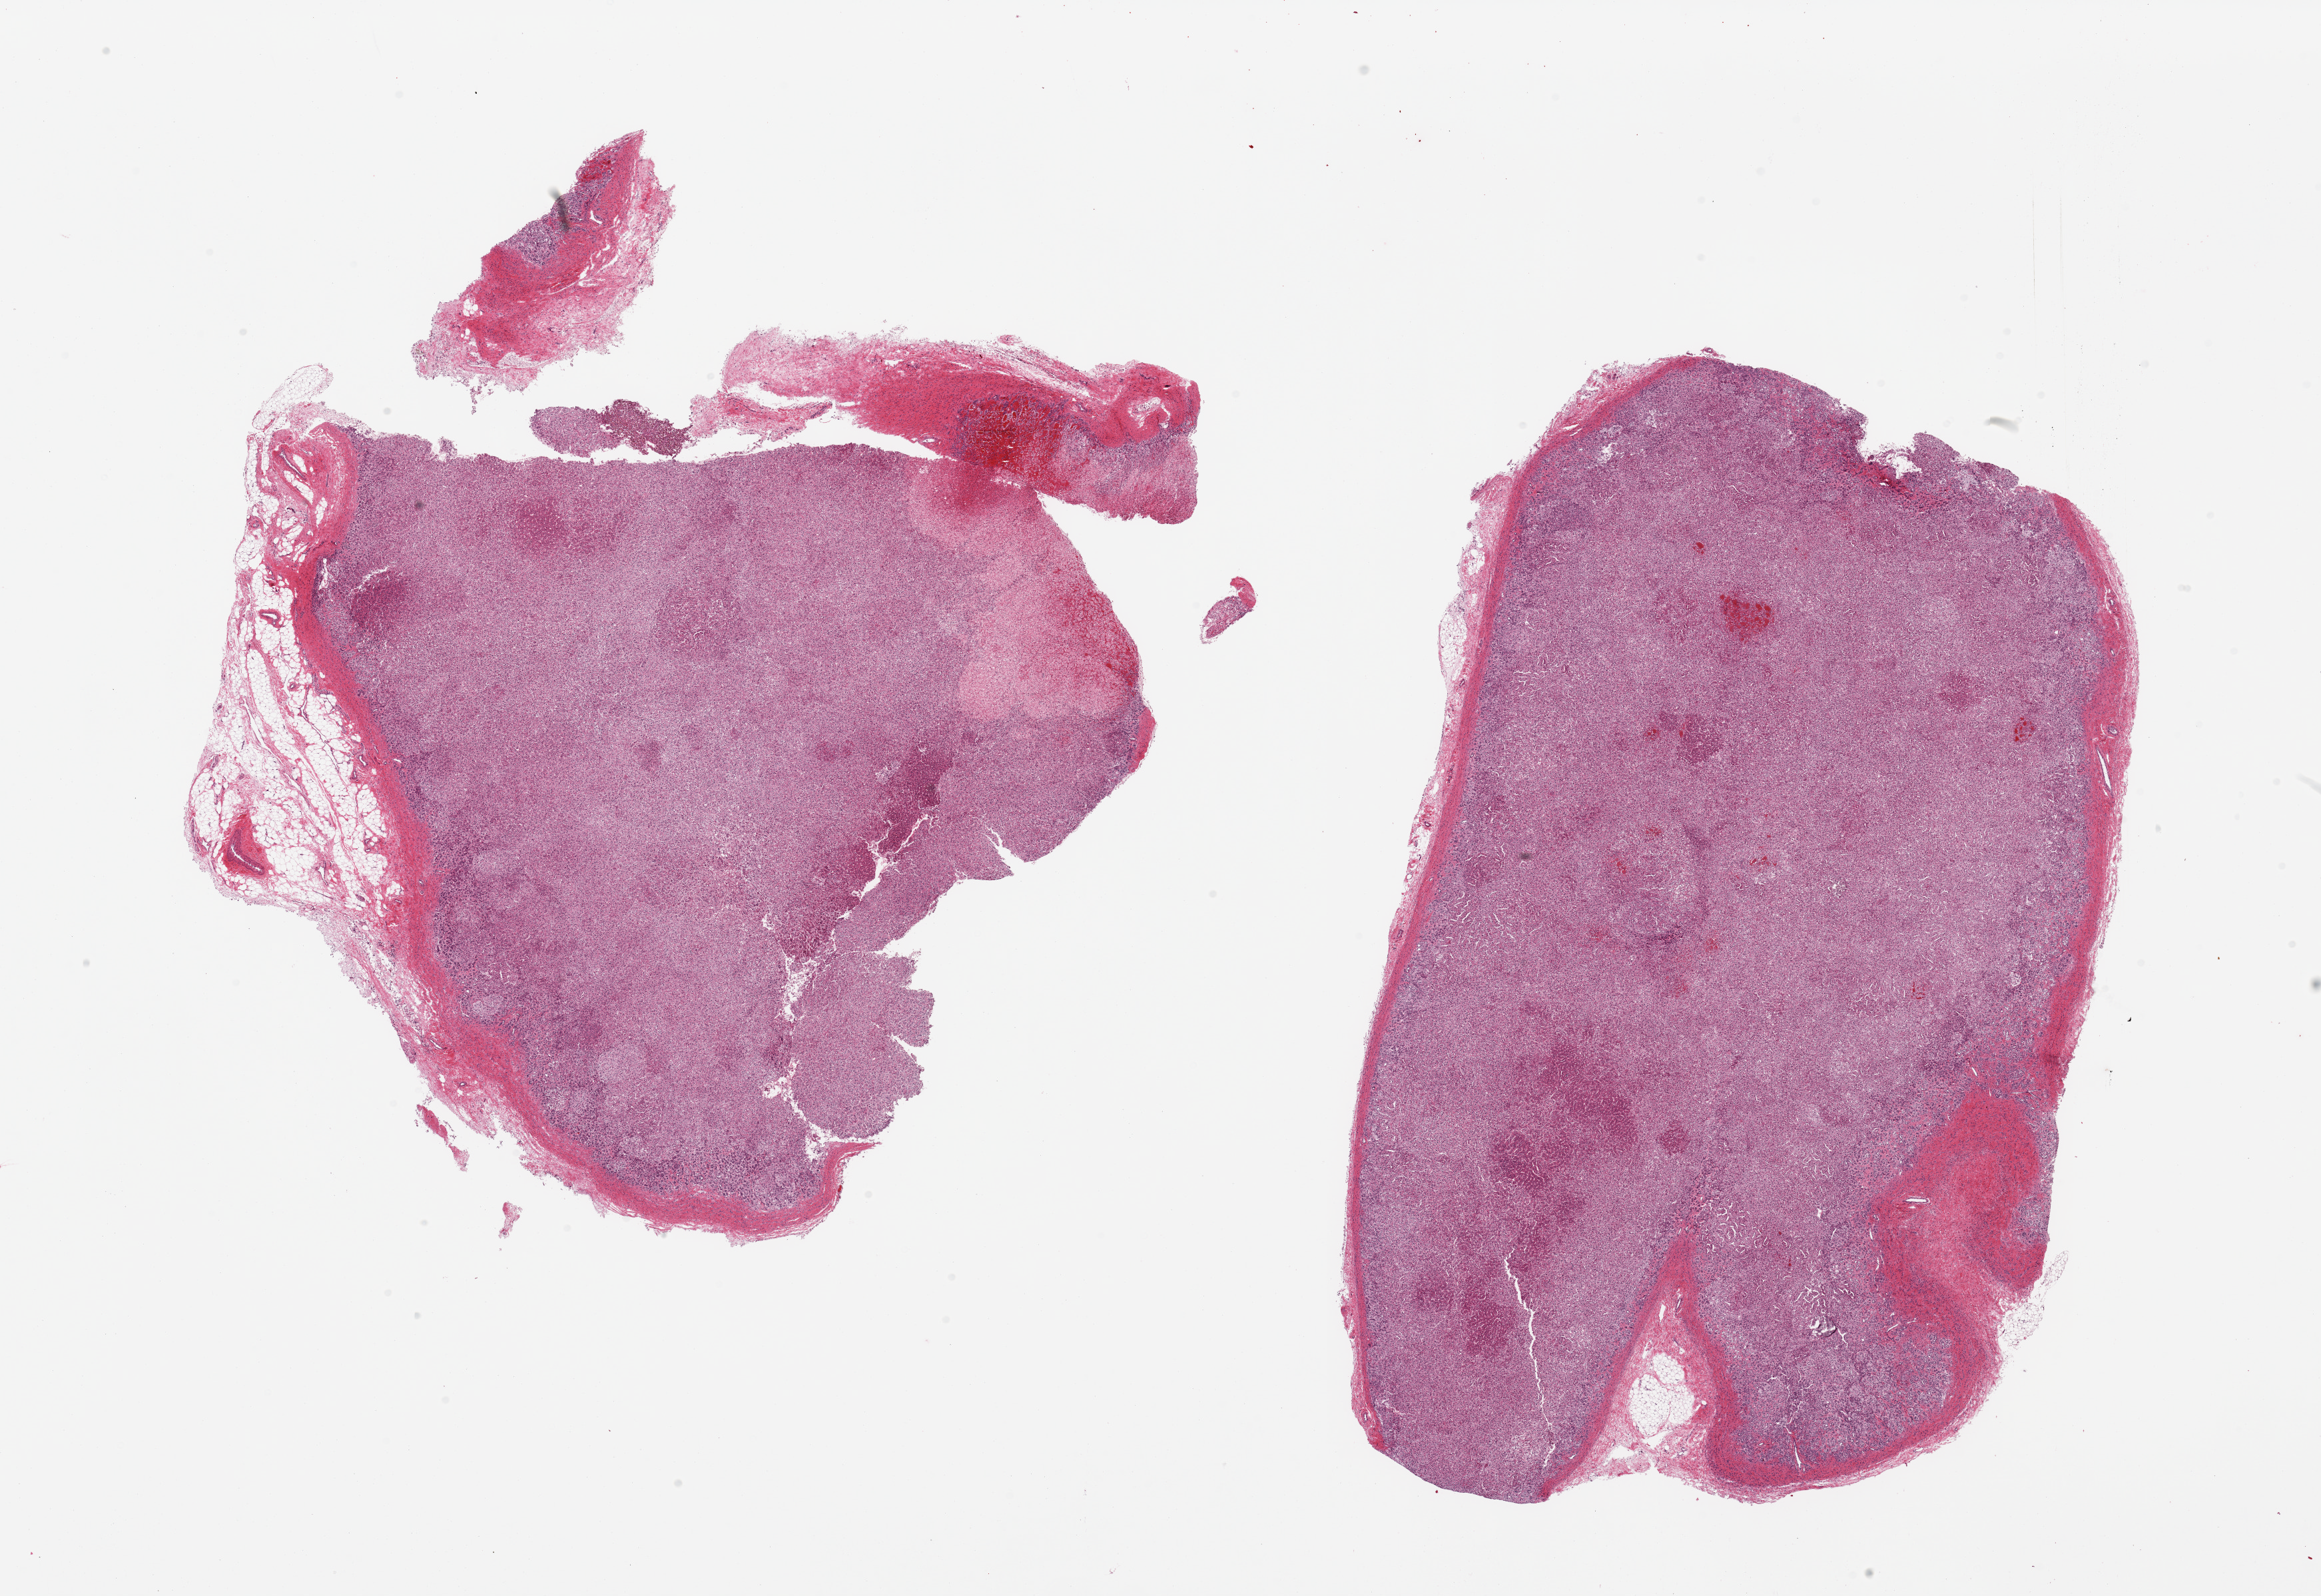
Hematoxylin and eosin (H&E) whole-slide image — whole scanned area (about 27.6 x 19.0 mm, from a 20x scan) shown as a low-resolution overview. PAXgene-fixed, paraffin-embedded tissue. Section of adrenal gland (target tissue). Tissue donor sample. Donor sex: male.
• pathologist's review note for this sample: 2 pieces; minimal attachment of fat, focal hemorrhage